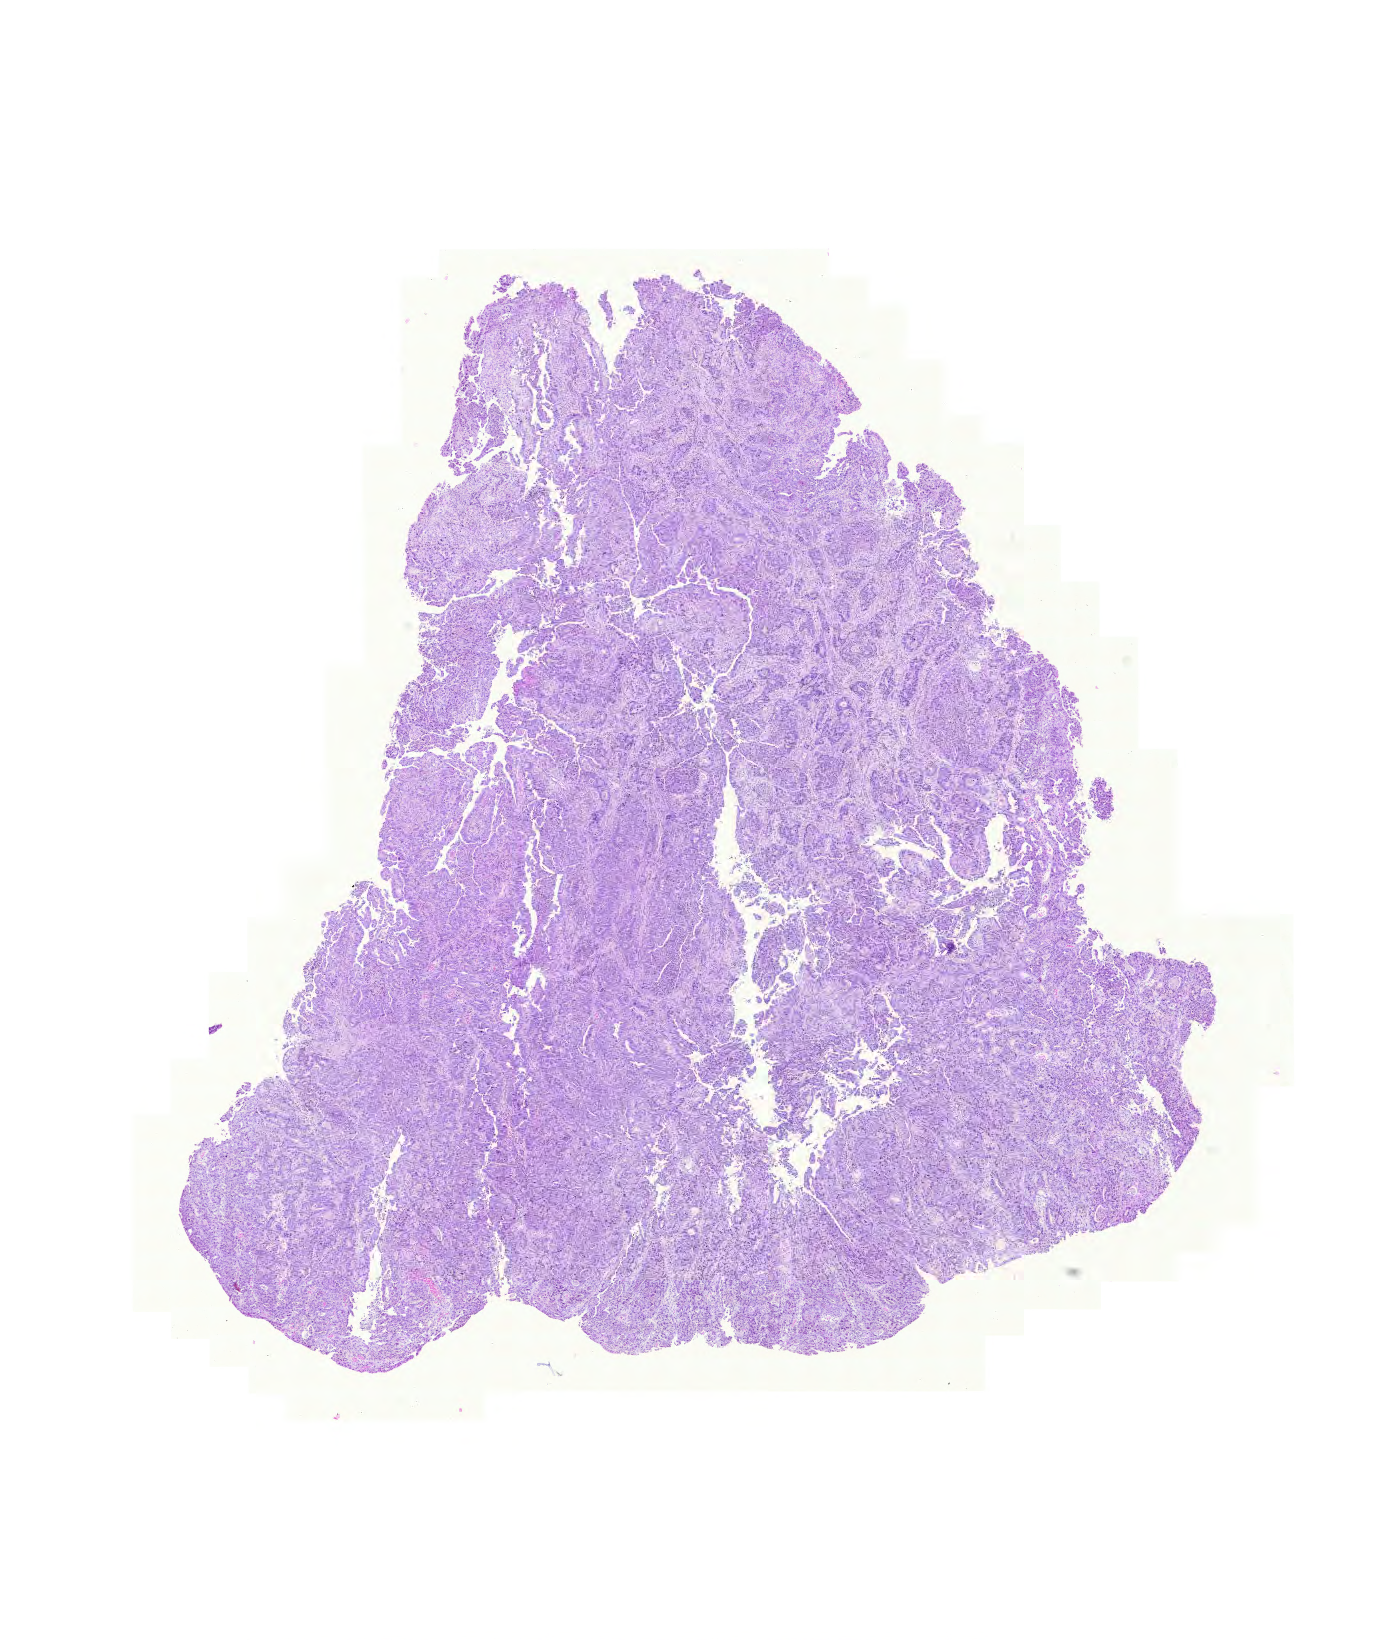
Digitized H&E tissue section (whole slide), low-resolution overview of the scanned area, about 10.4 x 12.2 mm (acquisition: 20x scan), formalin-fixed paraffin-embedded (FFPE) diagnostic section, sample: primary tumour, stomach. Male patient; age at initial diagnosis 79 years. Histologic grade: G2 (moderately differentiated).
Diagnosis: Adenocarcinoma, NOS (gastric antrum). AJCC pathologic stage: IIIB (6th edition).